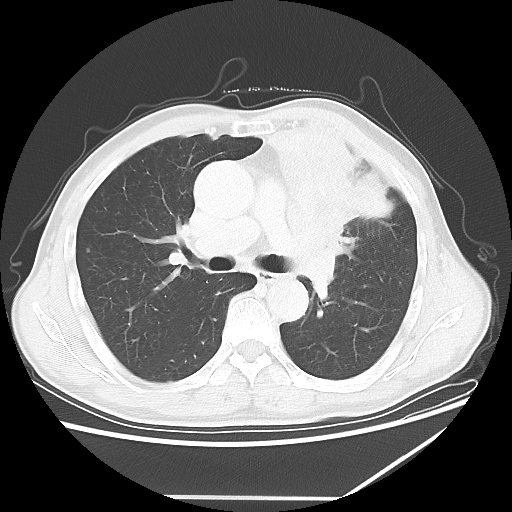
Chest CT, one axial slice; position 38 of 64 along the scan axis; 100 kVp; lung window (W 1500 / L -600 HU); 5 mm slice thickness; 512 × 512 image matrix, field of view 383 × 383 mm. Male patient, age 64 years. Case-level facts recorded for this patient, not image findings: clinical TNM (as recorded): T1c N1 M1; histopathological grade: G2.
Outlined on this slice (rectangle marked by the reading radiologist):
- lung tumour (recorded histology: squamous cell carcinoma): bounding box (x1, y1, x2, y2) in pixels: (270, 117, 401, 286)